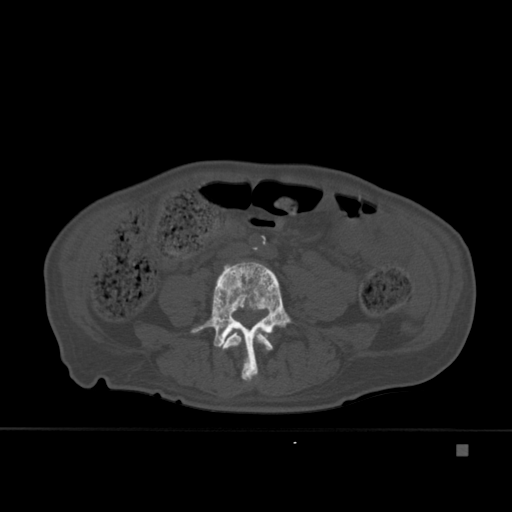
CT including the spine, one axial slice. Position 126 of 451 along the scan axis. Bone window (W 1800 / L 400 HU). 512 × 512 image matrix, field of view 378 × 378 mm. Male patient, age 75 years. Case-level facts recorded for this patient, not image findings: primary cancer: prostate.
Structures marked on this image (semi-automatically segmented with operator editing):
- L3 vertebra: box from (x=222, y=331) to (x=273, y=382) px
- L4 vertebra: (x=191, y=261)–(x=291, y=382)